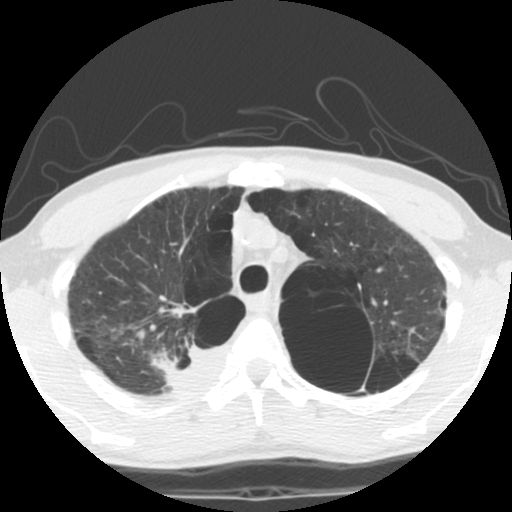
Low-dose screening chest CT, axial slice, second annual screen, lung window (W 1500 / L -600 HU), standard (soft-tissue) reconstruction kernel (STANDARD), slice 90 of 119 in the series, 512 × 512 image matrix. Male, age 62 years at enrolment. Current smoker at enrolment.
Lesion marked by an expert reader, bounding box [x1, y1, x2, y2] px = [126, 323, 219, 398]. Screening reader's record for this exam (one nodule recorded; not confirmed to be the boxed lesion): non-calcified nodule or mass ≥4 mm, 35 × 25 mm, soft tissue attenuation. Official screen result: positive, other. Lung cancer was diagnosed 14 days after this screen: non-small cell carcinoma, right upper lobe, poorly differentiated (G3), stage IA (AJCC 6th edition), 70 mm at pathology.